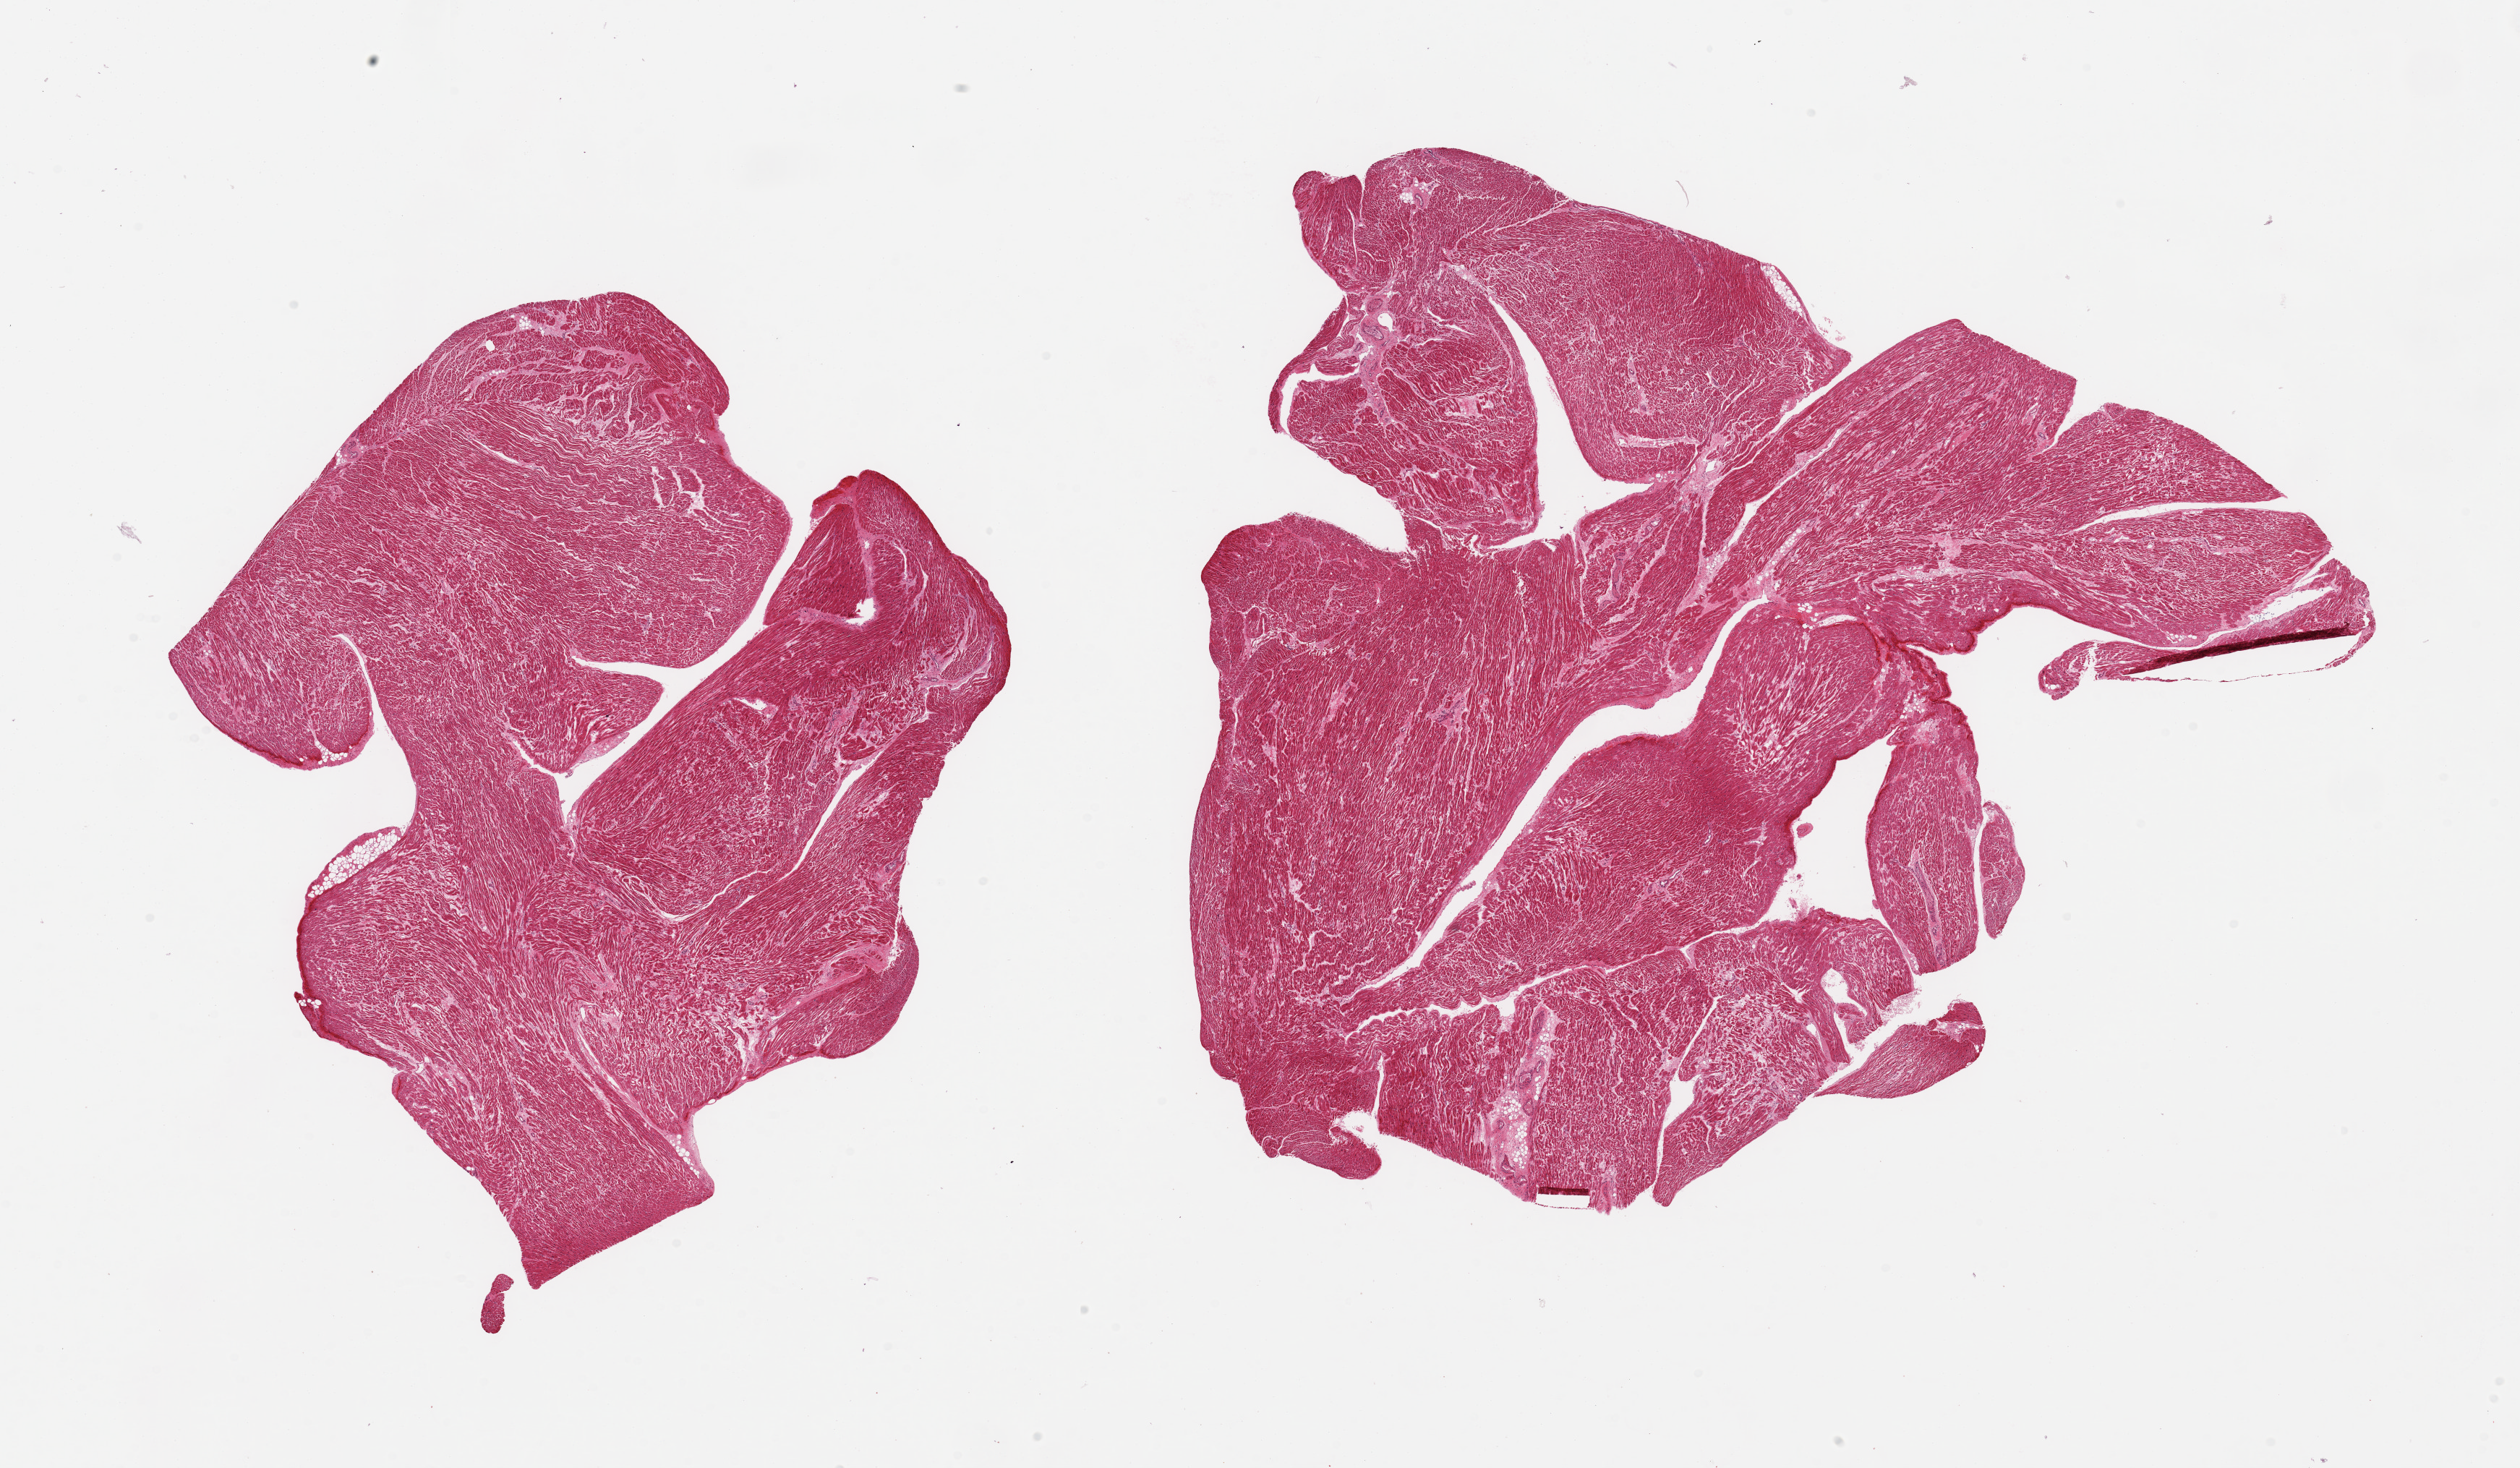
Whole-slide image, hematoxylin and eosin (H&E) stain, shown as a low-resolution overview of the whole scanned area (about 27.6 x 16.1 mm, slide scanned at 20x); PAXgene-fixed paraffin-embedded (PFPE) section; target tissue: auricular appendage; donor tissue sample. Donor sex: male.
Reviewer comment on this tissue sample: 2 pieces, no abnormalities.